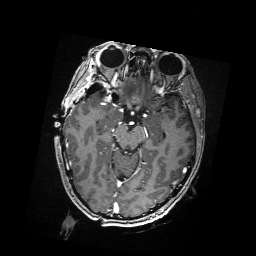
Brain MRI from a brain-tumour surgery series, one axial slice; position 109 of 176 along the scan axis; T1-weighted post-contrast; 1 mm slice thickness; 256 × 256 image matrix, field of view 256 × 256 mm. Case-level facts recorded for this patient, not image findings: histopathology: Metastatic Carcinoma from Breast primary.
Structures marked on this image (manually delineated by an expert):
- residual tumour: bounding box <106,89,113,96> (left, top, right, bottom; pixels)